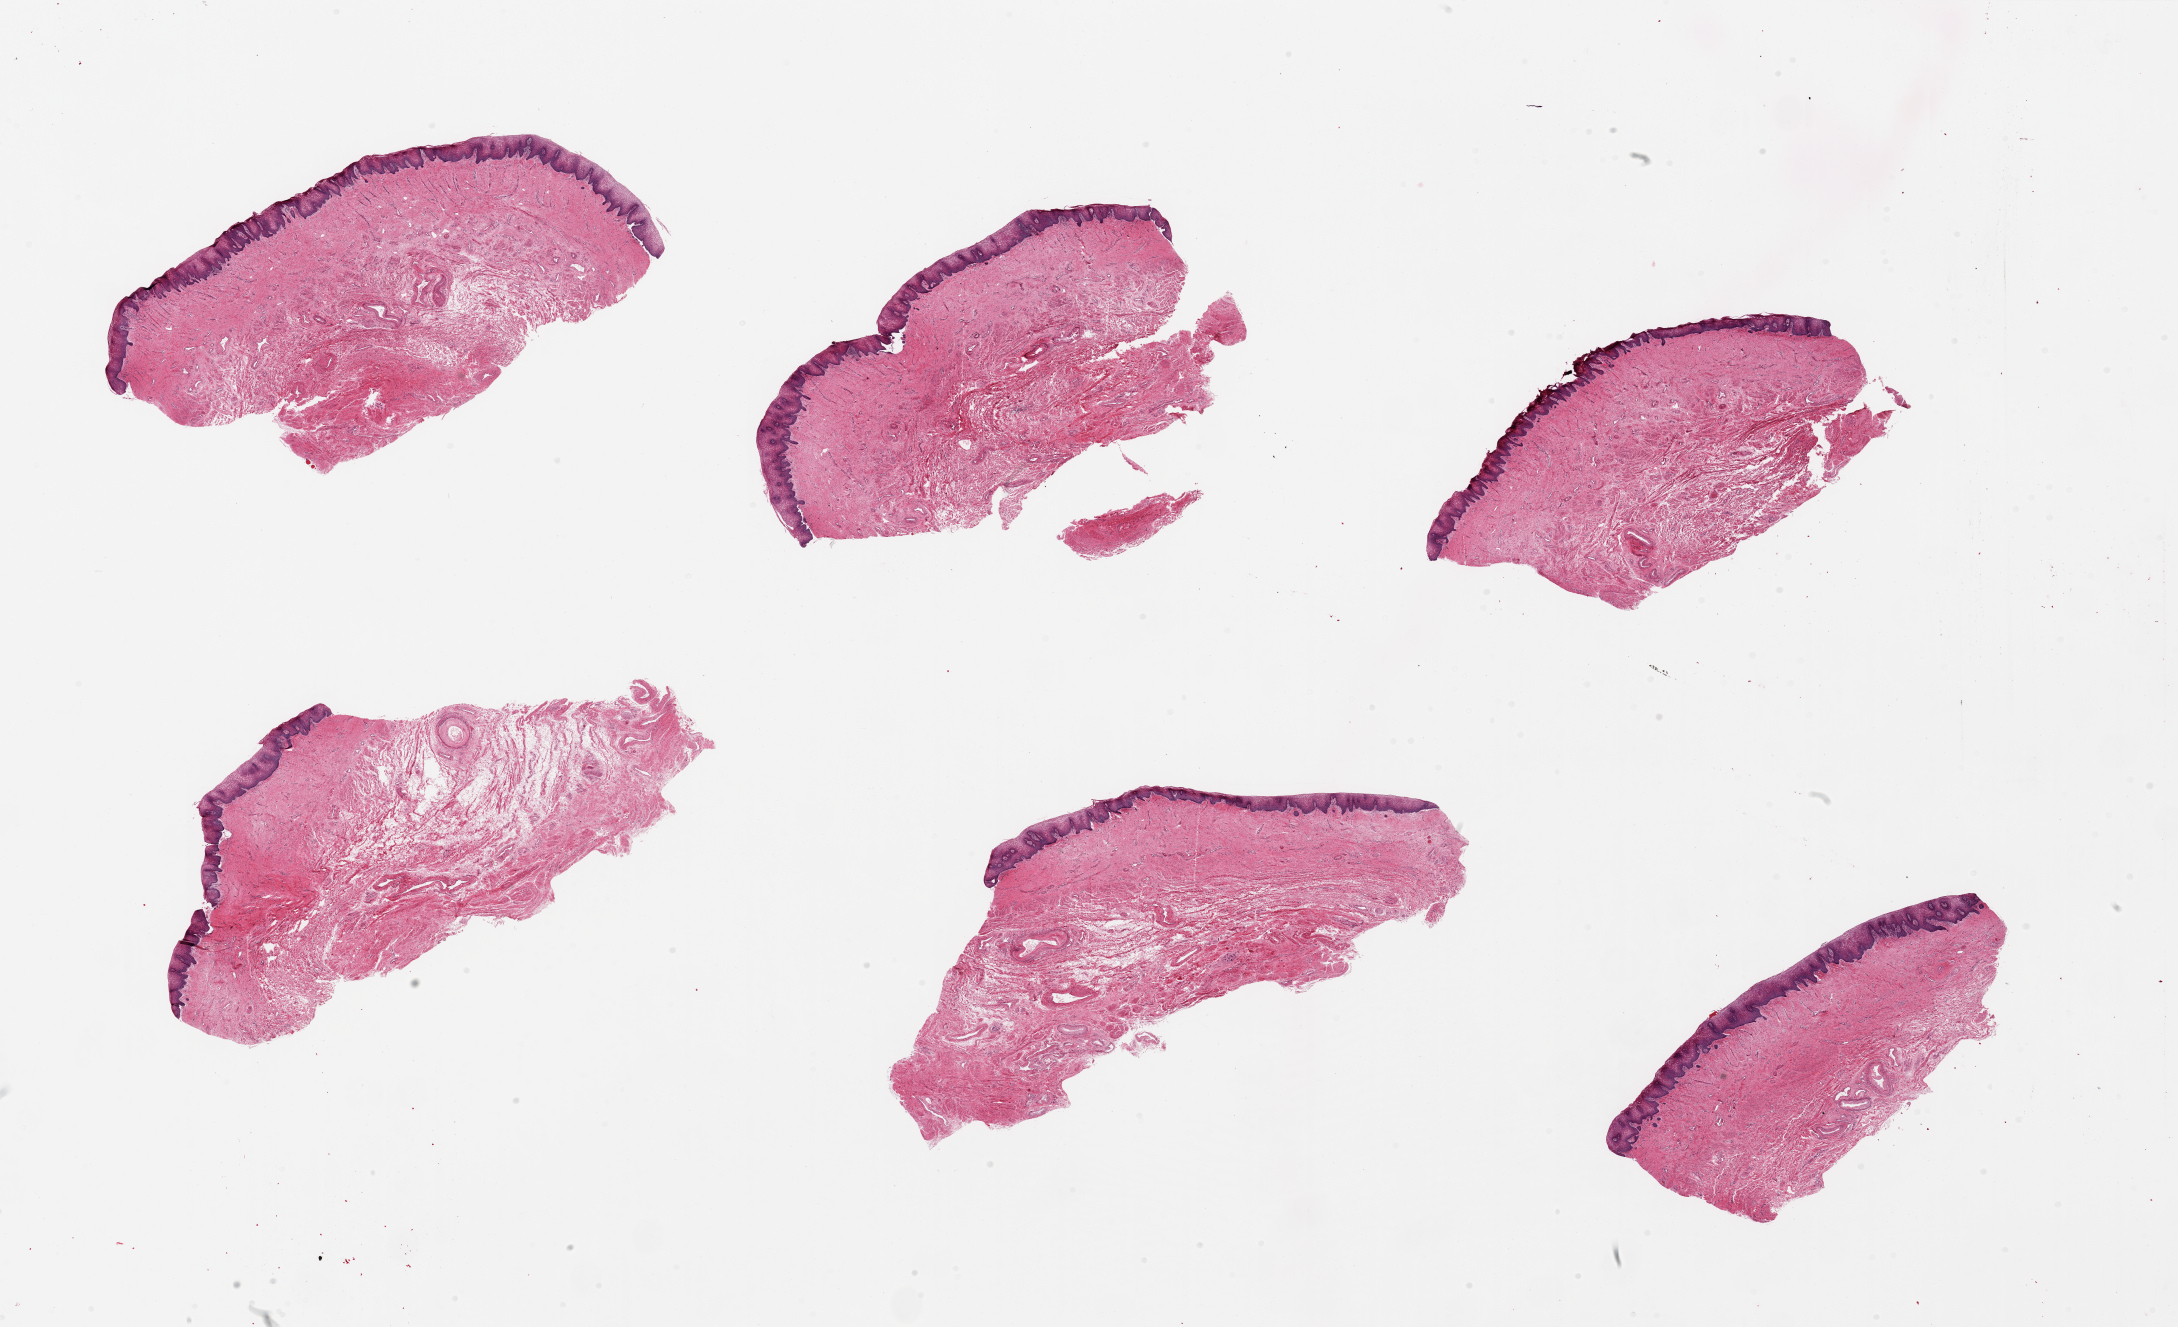
Whole-slide image, hematoxylin and eosin (H&E) stain, brightfield, a low-resolution overview of the entire scanned area, about 34.5 x 21.0 mm; PAXgene-fixed paraffin-embedded (PFPE) section; target tissue: vagina; donor tissue sample. Donor sex: female.
Reviewer comment on this tissue sample: 6 pieces.